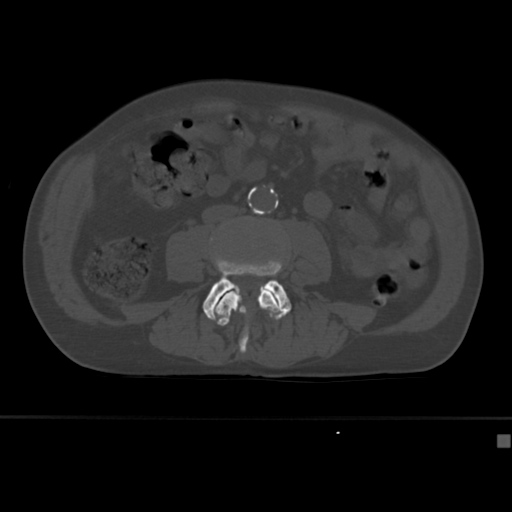
CT including the spine, one axial slice; slice 115 of 430 in the series (ordered by position); 120 kVp; bone window (W 1800 / L 400 HU); 1.5 mm slice thickness; 512 × 512 image matrix, field of view 337 × 337 mm. Male patient, age 64 years. Case-level facts recorded for this patient, not image findings: primary cancer: uterus.
Structures marked on this image (semi-automatic segmentation, software-assisted and operator-edited):
- L3 vertebra: bounding box <216,291,281,356> (left, top, right, bottom; pixels)
- L4 vertebra: <203,258,291,326>